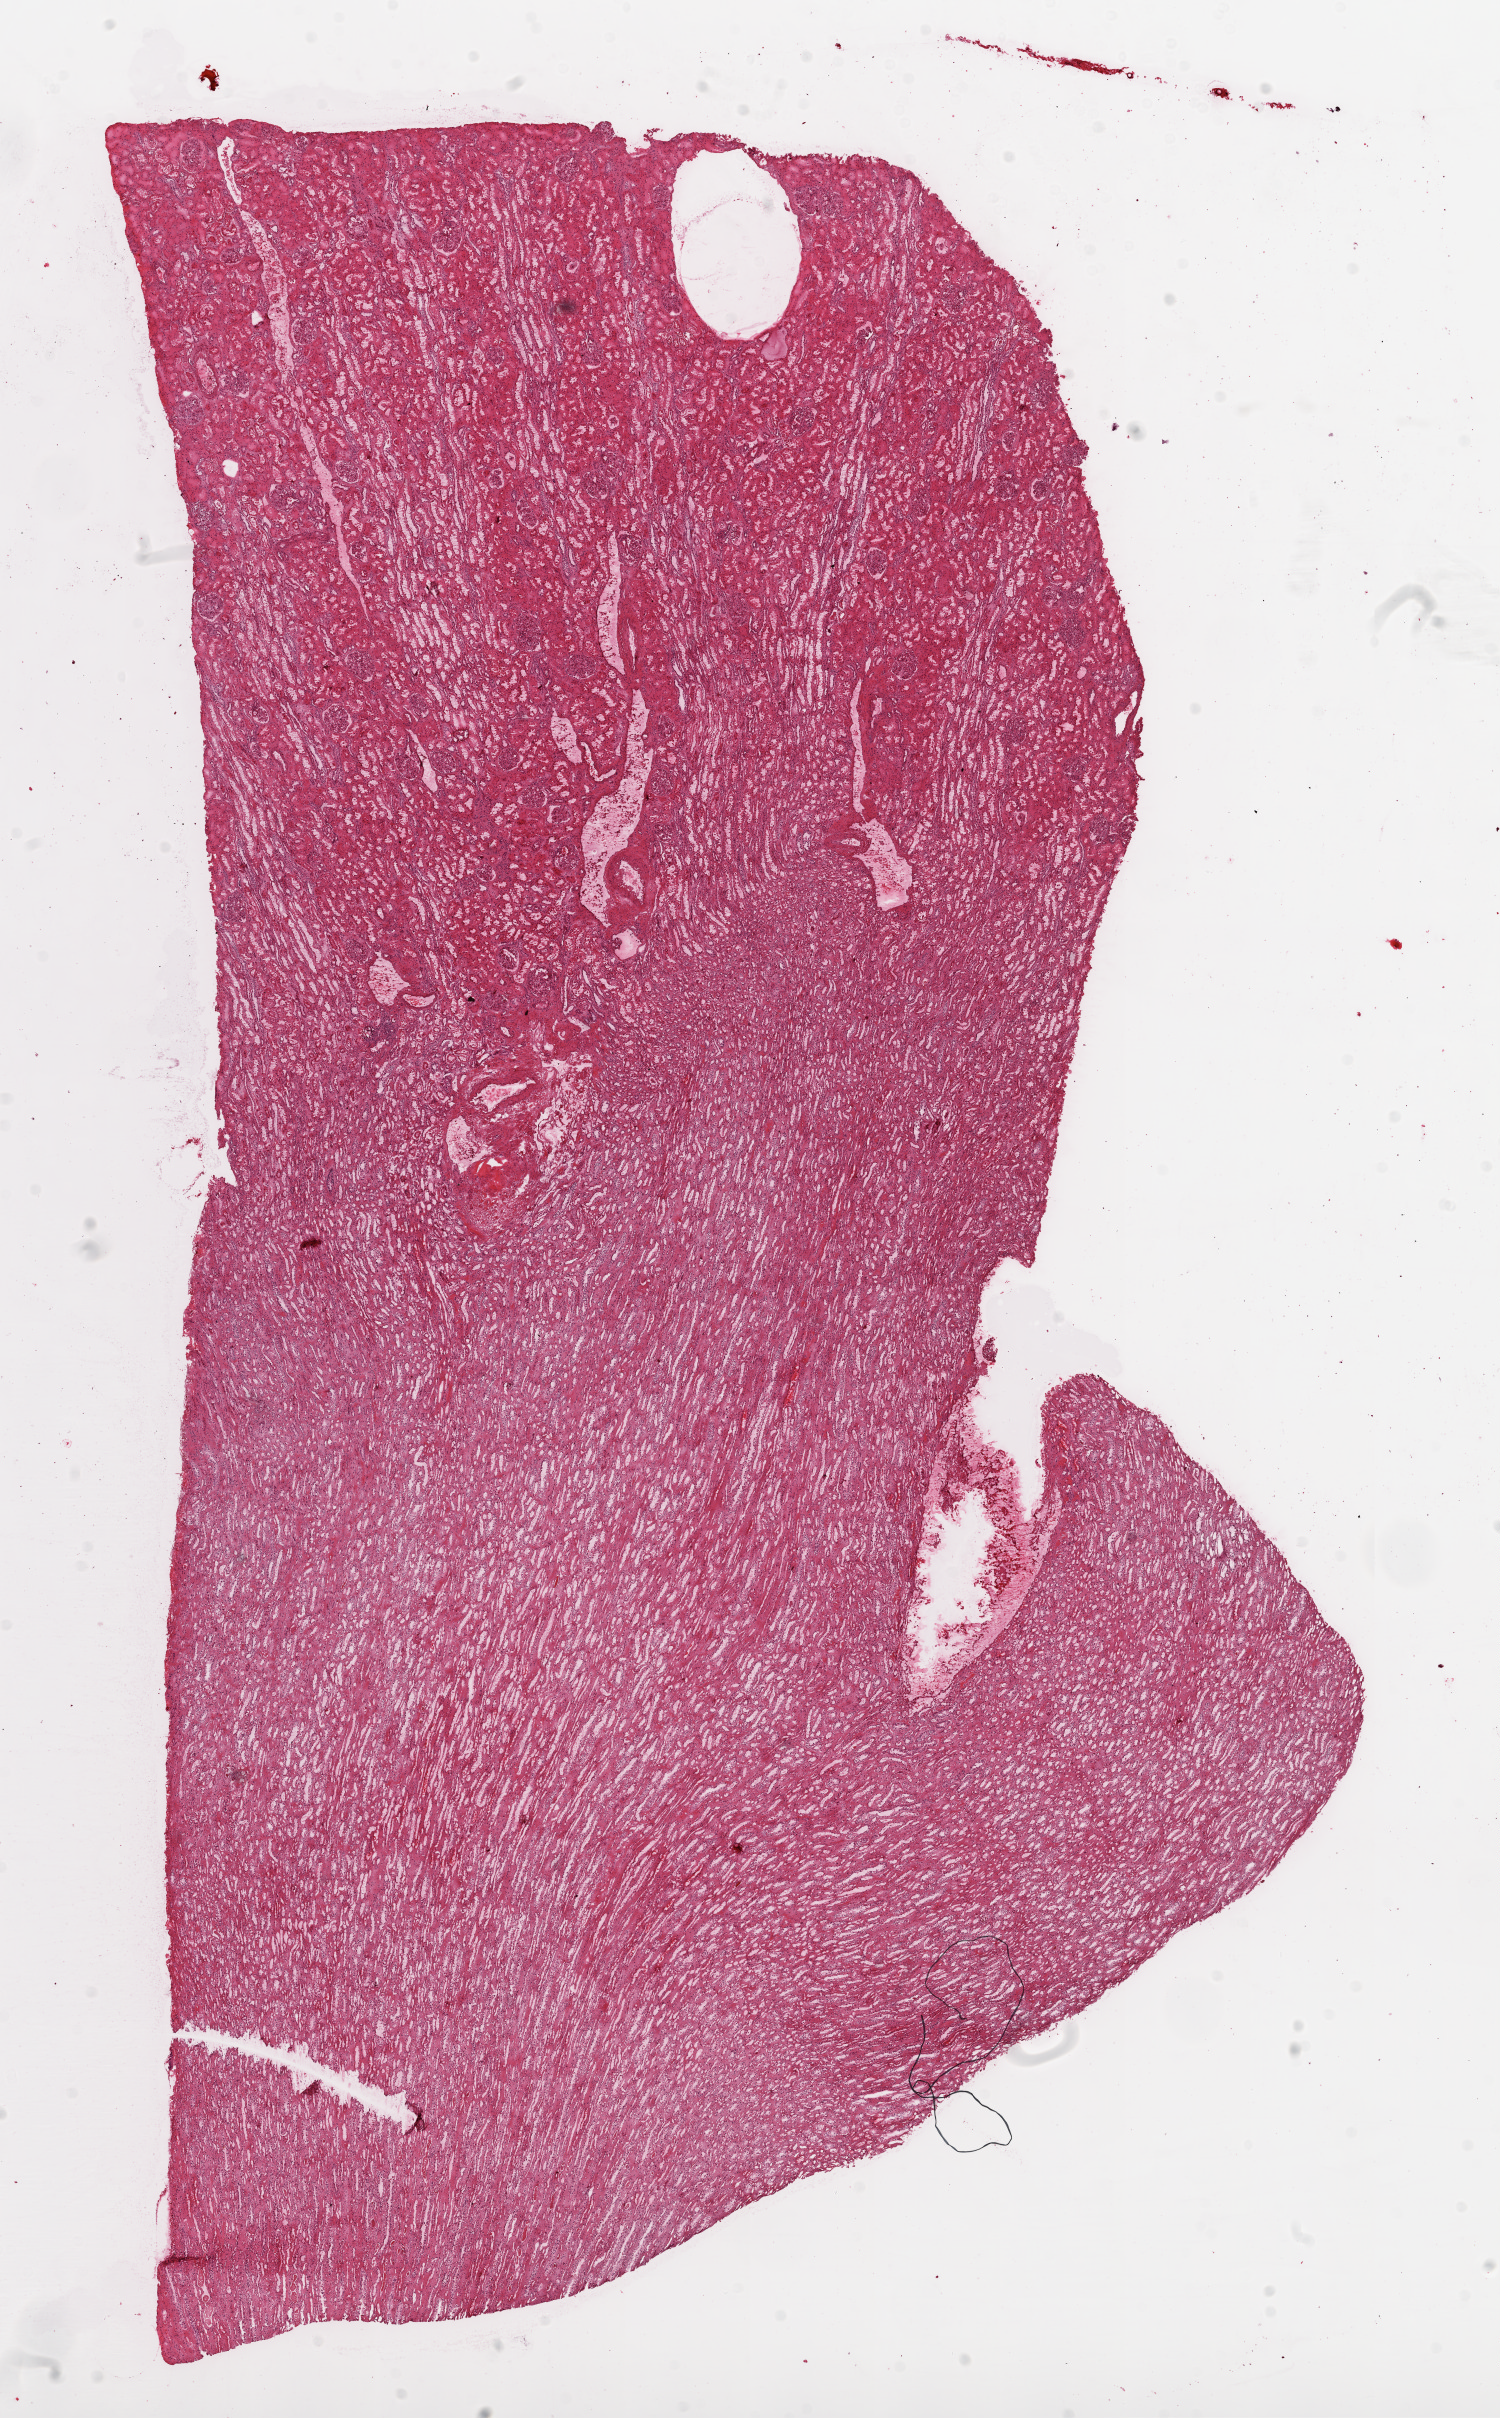
Digitized H&E-stained tissue section (whole slide) — a low-resolution overview of the entire scanned area, about 12.0 x 19.4 mm (slide scanned at 20x), frozen section from the top of the tissue portion, sample: solid tissue normal (non-tumour tissue), kidney. Male, age 49 years at initial diagnosis.
• this section: solid tissue normal sample (biorepository sample class)
• patient diagnosis: Clear cell adenocarcinoma, NOS